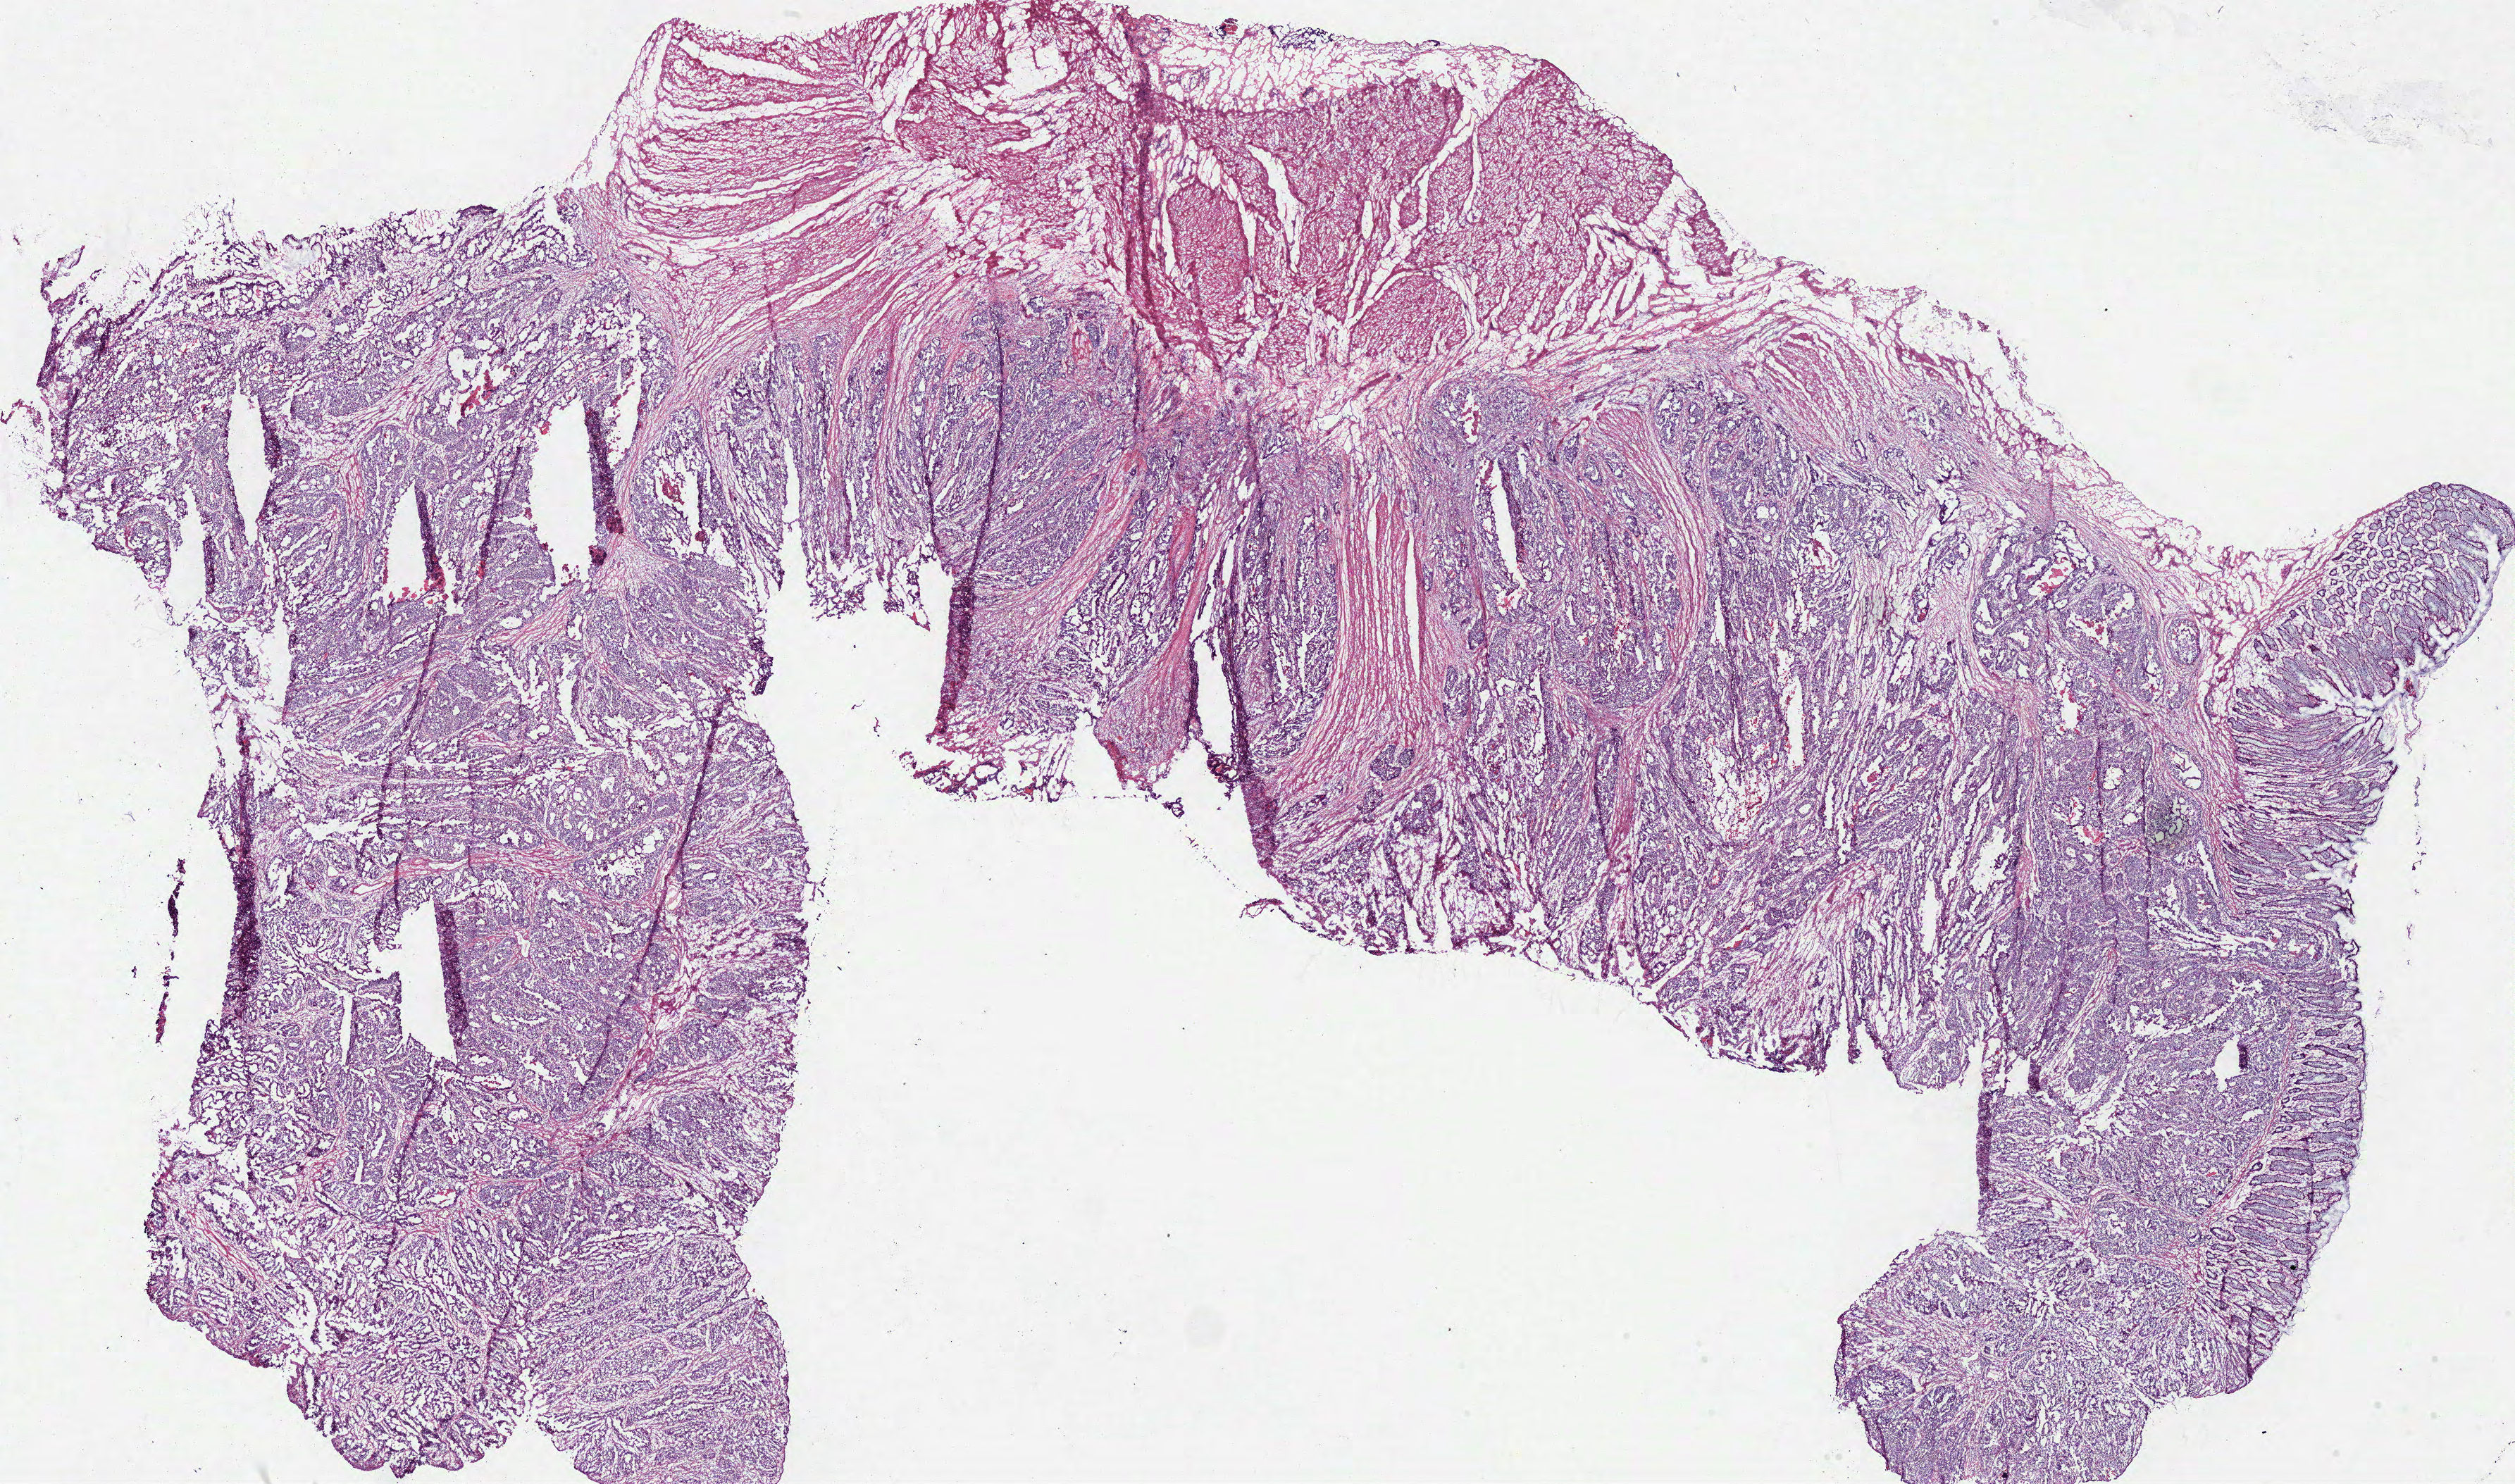
Hematoxylin and eosin (H&E) stained whole-slide image — a low-resolution overview of the entire scanned area, about 28.1 x 16.6 mm. Pathologist review of this section (percent, as recorded): tumour cells 75%, tumour nuclei 80%, normal cells 20%, necrosis 5%. Inflammatory infiltration, as recorded: lymphocyte infiltration 10%, neutrophil infiltration 3%.
Specimen: frozen section from the bottom of the tissue portion; sample: primary tumour, rectum.